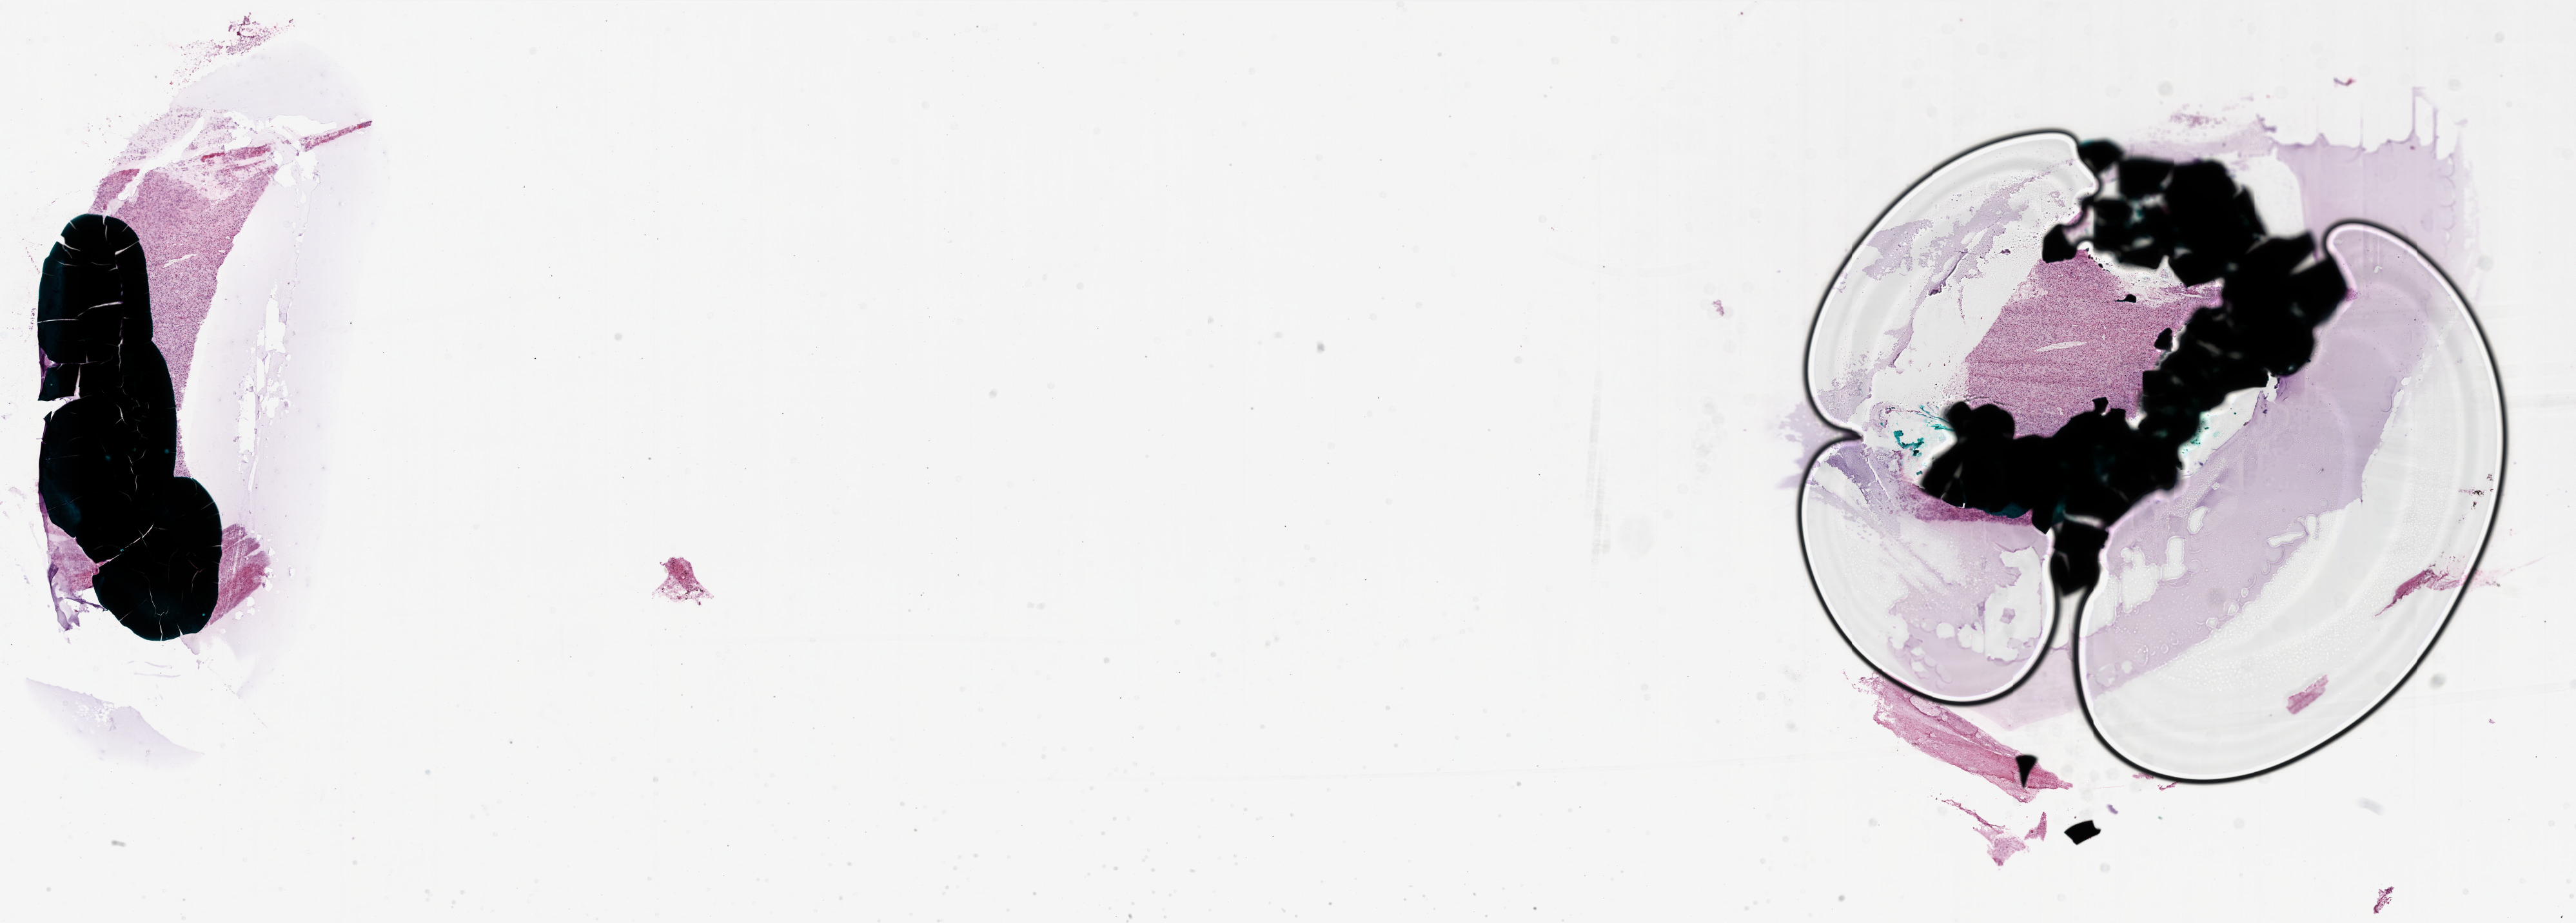
Digitized H&E tissue section (whole slide), a low-resolution overview of the entire scanned area, about 32.0 x 11.5 mm. Frozen section from the bottom of the tissue portion. Sample: primary tumour, brain. Male, age 43 years at initial diagnosis. Composition of this section per pathologist review: tumour cells 80%, tumour nuclei 95%, normal cells 0%, stromal cells 15%, necrosis 5%. Inflammatory infiltration, as recorded: lymphocyte infiltration 0%, monocyte infiltration 0%, neutrophil infiltration 0%.
Histologic diagnosis: Glioblastoma.